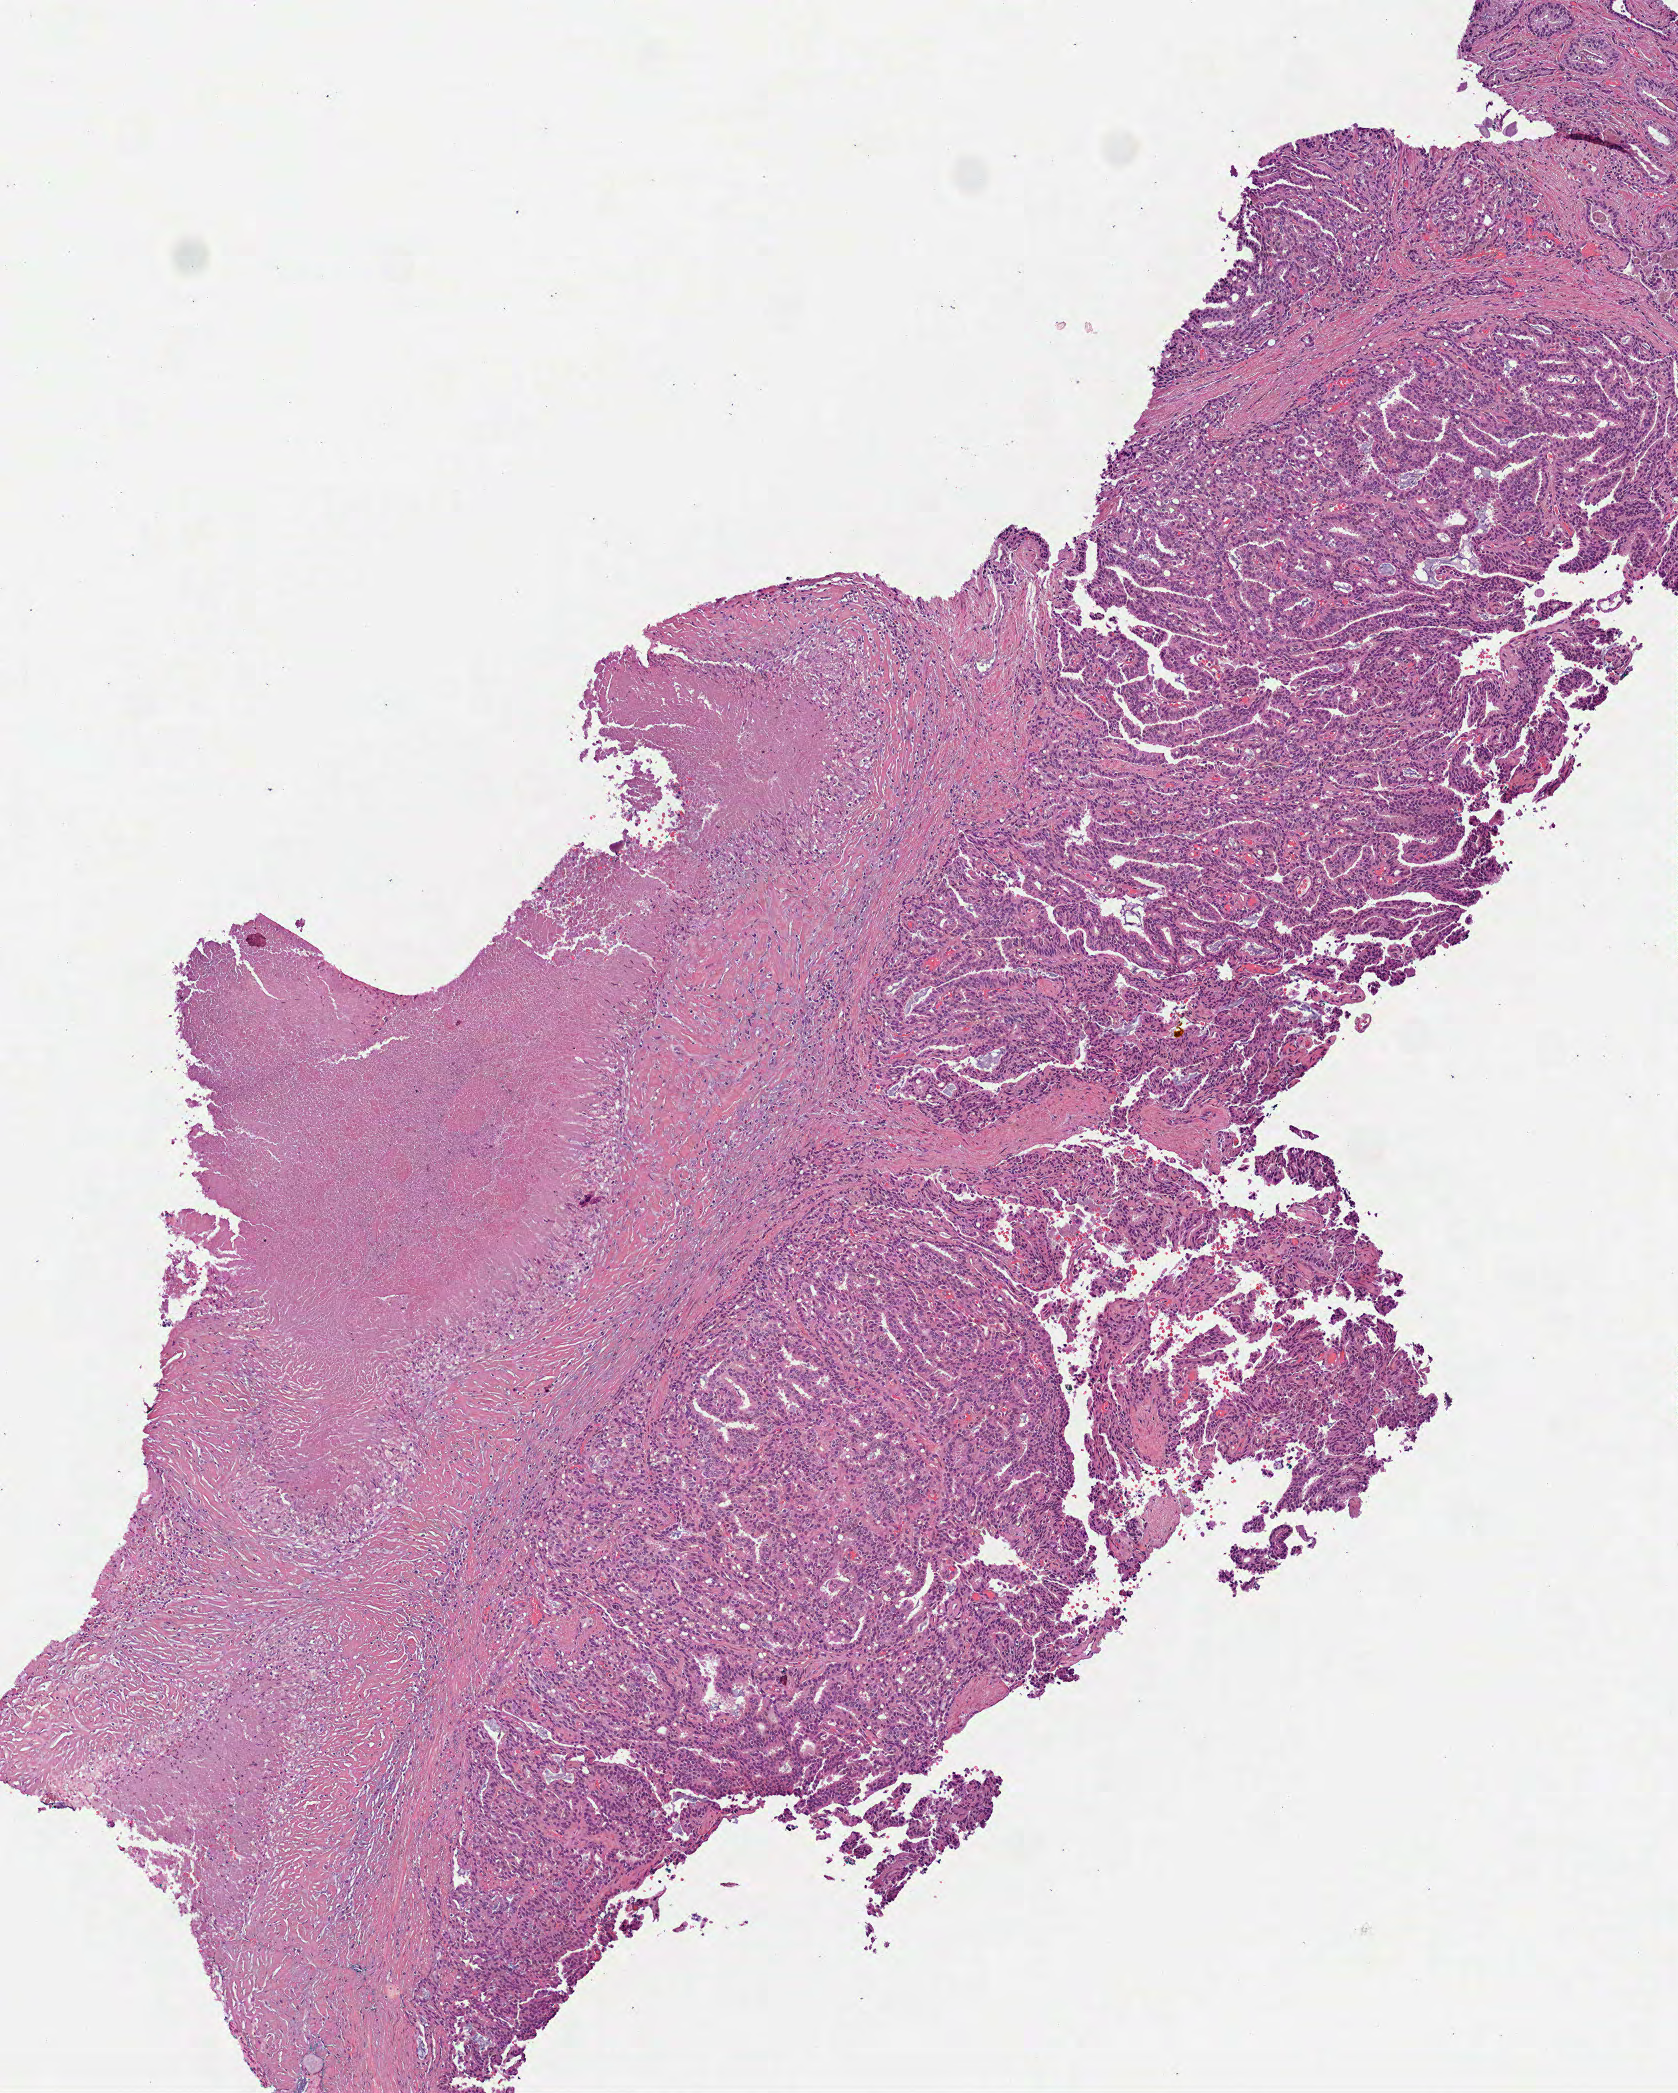
Whole-slide histology image, H&E-stained — low-resolution overview of the scanned area, about 3.4 x 4.2 mm, formalin-fixed paraffin-embedded (FFPE) diagnostic section, primary tumour sample from the prostate. Patient: male, age at initial diagnosis 66 years. Gleason score: 7 (3+4).
* lymph nodes positive (case pathology): 0 of 2 examined
* pathologic diagnosis: Acinar cell carcinoma (prostate gland)
* laterality: right